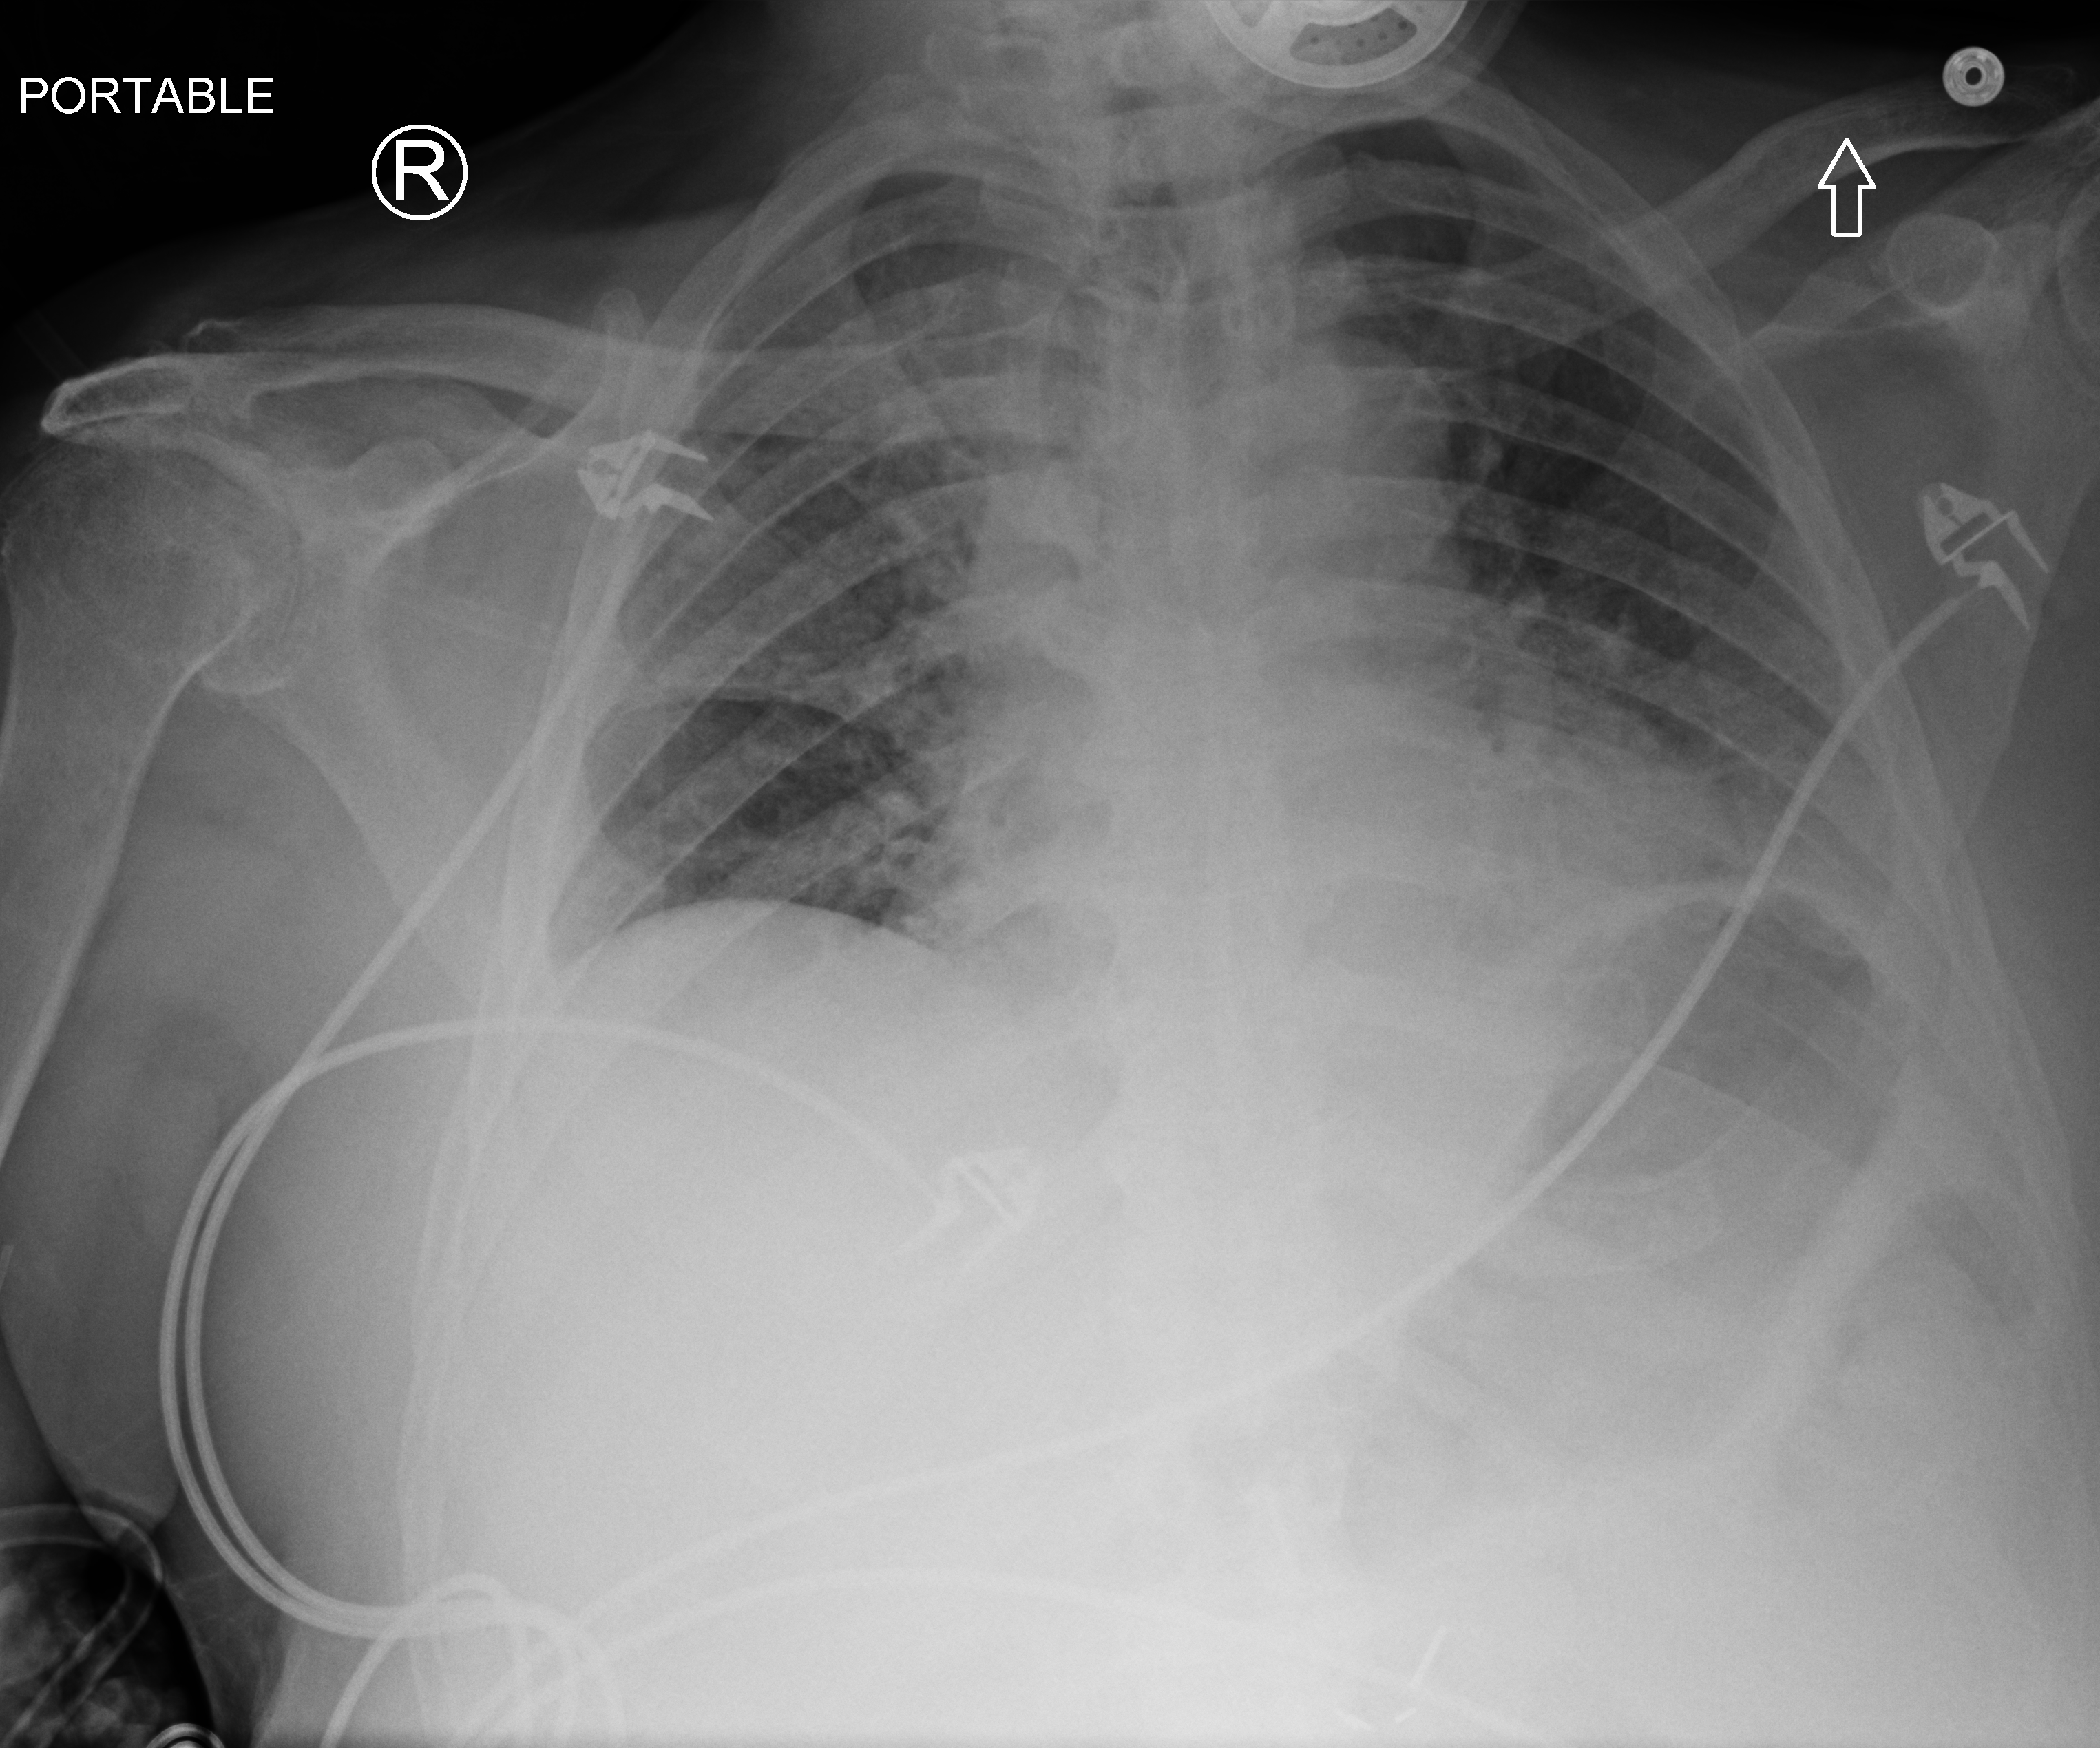
Portable chest radiograph; anteroposterior (AP) projection. Patient hospitalised with COVID-19; male, aged 75–90 years.
Admission-level facts for this patient (not findings on this image; timing relative to this image not recorded): diabetes (admission record): no; admitted to intensive care during this hospital stay: yes.